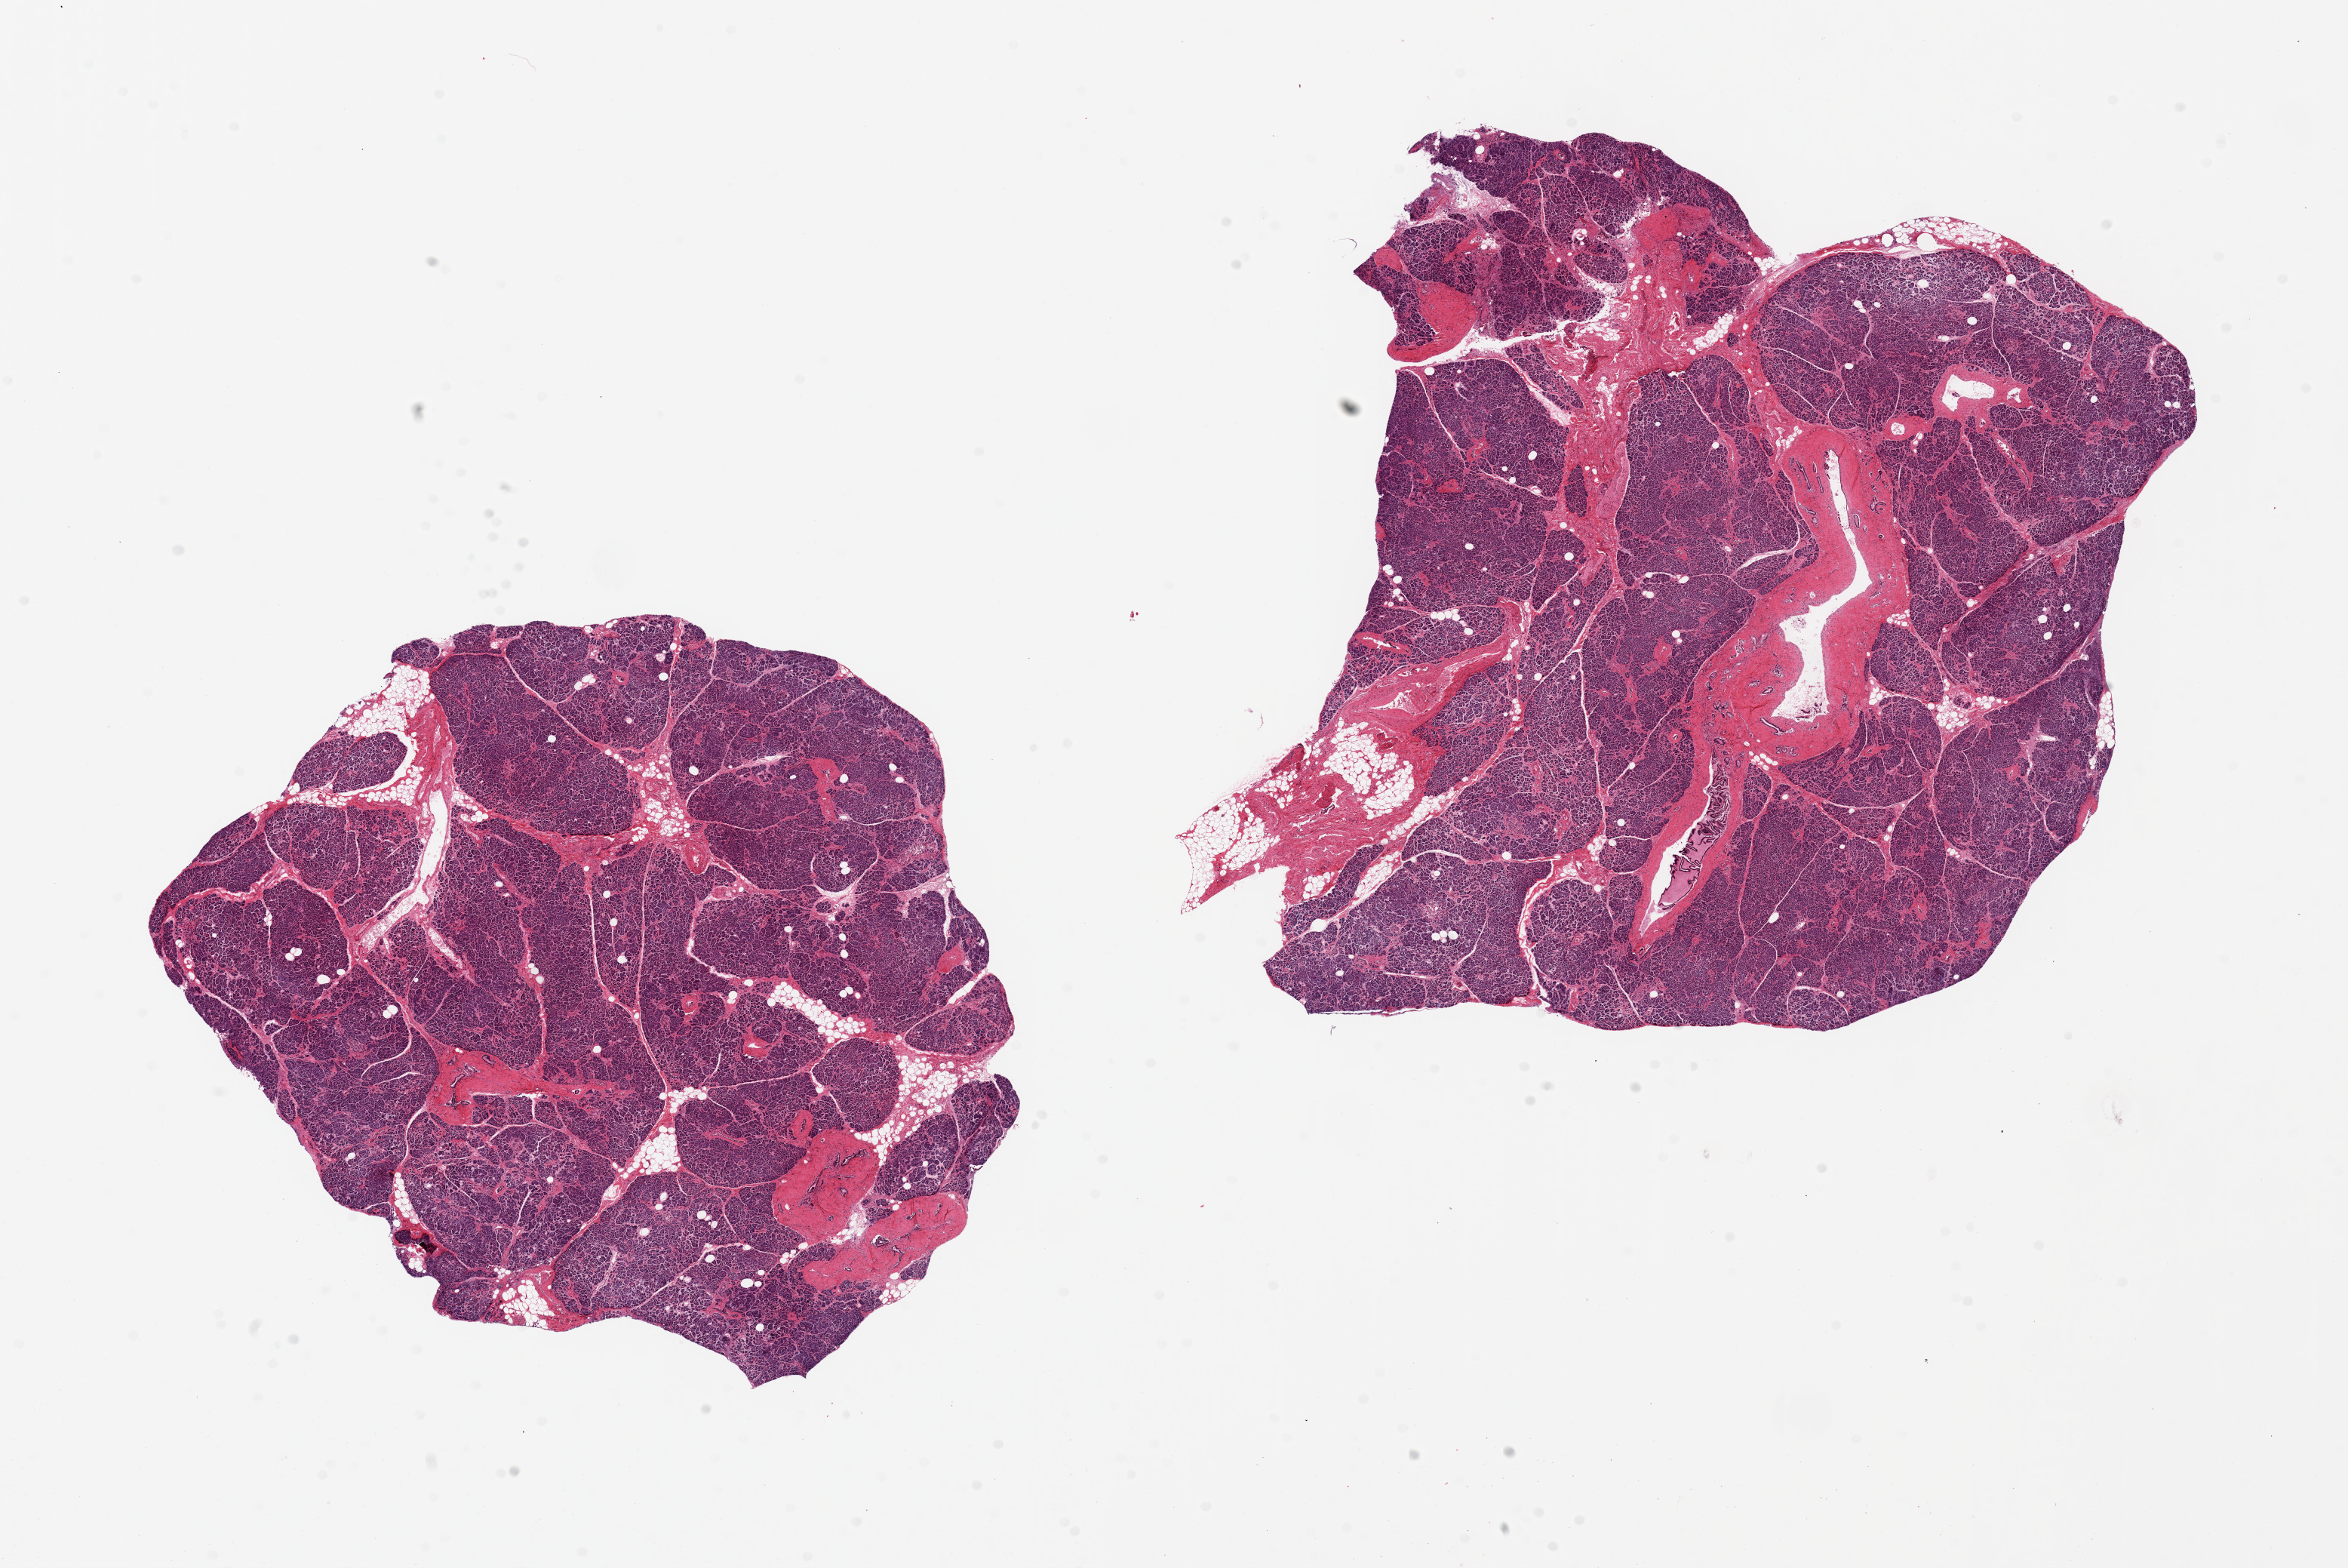
Digitized haematoxylin and eosin-stained section, whole scanned area (about 24.6 x 16.4 mm, from a 20x scan) shown as a low-resolution overview. PAXgene-fixed paraffin-embedded (PFPE) section. Sampled site (target tissue): pancreas. Donor tissue sample. Donor sex: female.
- reviewer comment on this tissue sample: 2 pieces ~8x8mm, Islets visible, poorly preserved, pathcy saponification